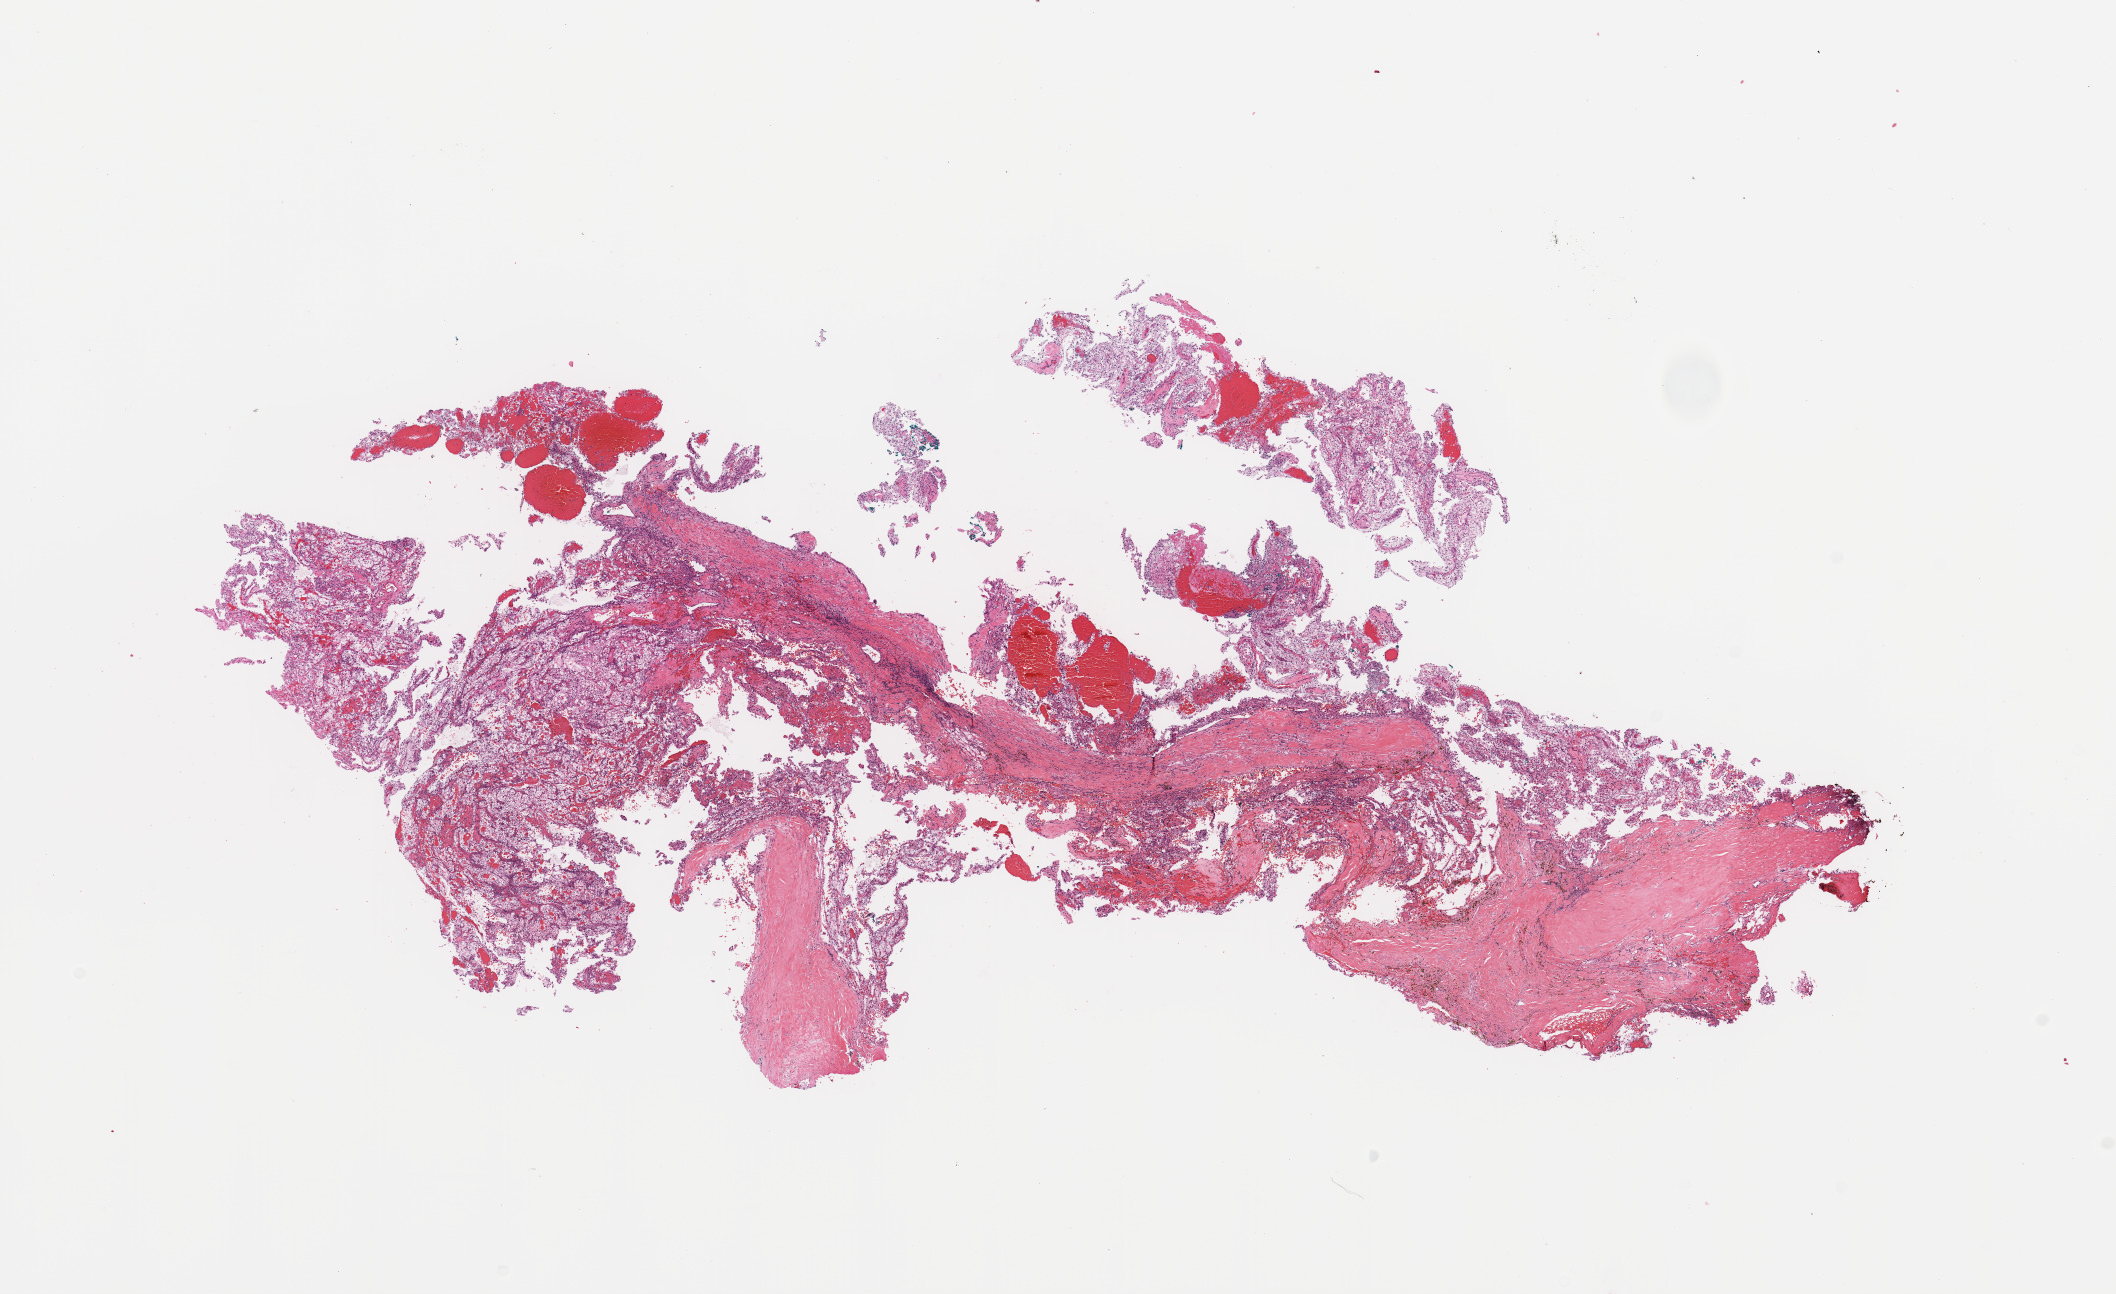
Digitized H&E-stained tissue section (whole slide) — a low-resolution overview of the entire scanned area, about 16.7 x 10.2 mm. Tumour tissue sample, kidney. Male, 63 y/o. Histologic grade: G2 (moderately differentiated).
* AJCC pathologic stage: I
* primary tumour site (as recorded): lower pole
* histologic diagnosis: Renal cell carcinoma, NOS